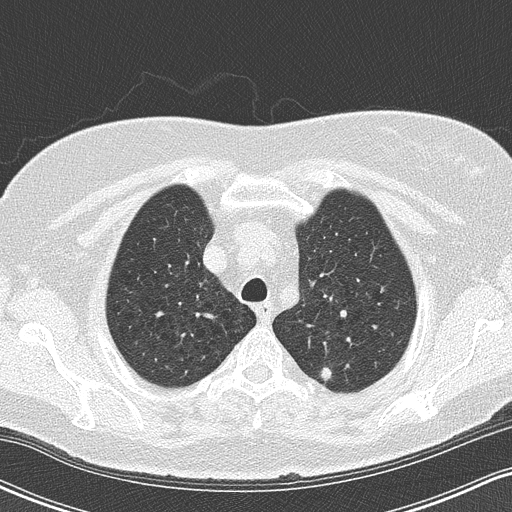
Low-dose screening chest CT, axial slice; third screening round (two years after baseline); lung window (W 1500 / L -600 HU); 2 mm slice thickness; lung (sharp) reconstruction kernel (B50f); 512 × 512 image matrix, field of view 320 × 320 mm. Female participant, aged 65 years at enrolment.
• Lesion marked by an expert reader, bounding box (x1, y1, x2, y2) in pixels: (307, 354, 349, 393).
• The exam's reader record, not a measurement of the box and not confirmed to be the same lesion: non-calcified nodule or mass ≥4 mm, left upper lobe, 8 × 6 mm, pre-existing on the prior screen: yes.
• Official screen result: positive, no significant change: stable abnormalities potentially related to lung cancer, unchanged since the prior screening exam.
• Later outcome: lung cancer diagnosed 103 days after this screen — adenocarcinoma, NOS, left upper lobe, moderately differentiated (G2), stage IA (AJCC 6th edition), 8 mm at pathology.